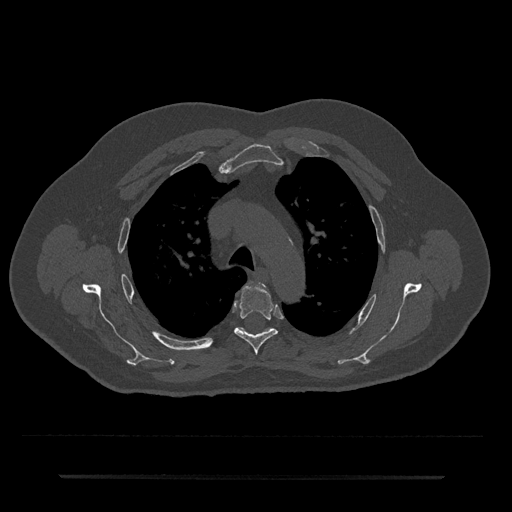
CT including the spine, one axial slice. Reconstruction kernel Br40s/3. 120 kVp. Bone window (W 1800 / L 400 HU). 512 × 512 image matrix, field of view 437 × 437 mm. Patient: male, 69 years. From the clinical record (not read from this slice): primary cancer: prostate.
Outlined on this slice (semi-automatically segmented with operator editing):
- T4 vertebra: bounding box <234,285,277,354> (left, top, right, bottom; pixels)
- T5 vertebra: <237,327,272,332>